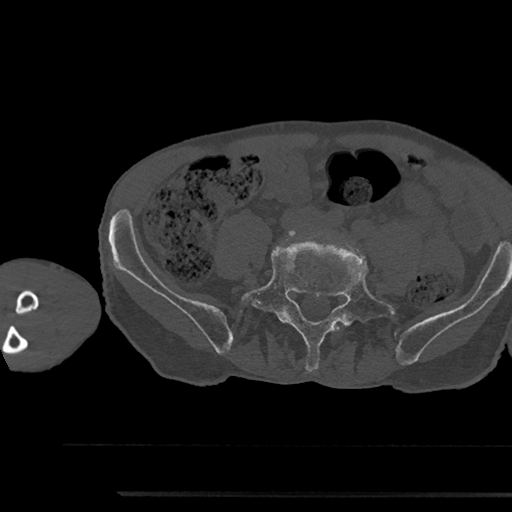
CT including the spine, one axial slice; slice 355 of 797 in the series (ordered by position); 120 kVp; bone window (W 1800 / L 400 HU); 0.5 mm slice thickness; 512 × 512 image matrix, field of view 367 × 367 mm. Male patient, age 79 years. Case-level facts recorded for this patient, not image findings: primary cancer: prostate.
Annotated regions visible in this slice (semi-automatic segmentation, software-assisted and operator-edited):
- L4 vertebra: bounding box [x1, y1, x2, y2] px = [335, 326, 340, 331]
- L5 vertebra: [241, 245, 397, 371]